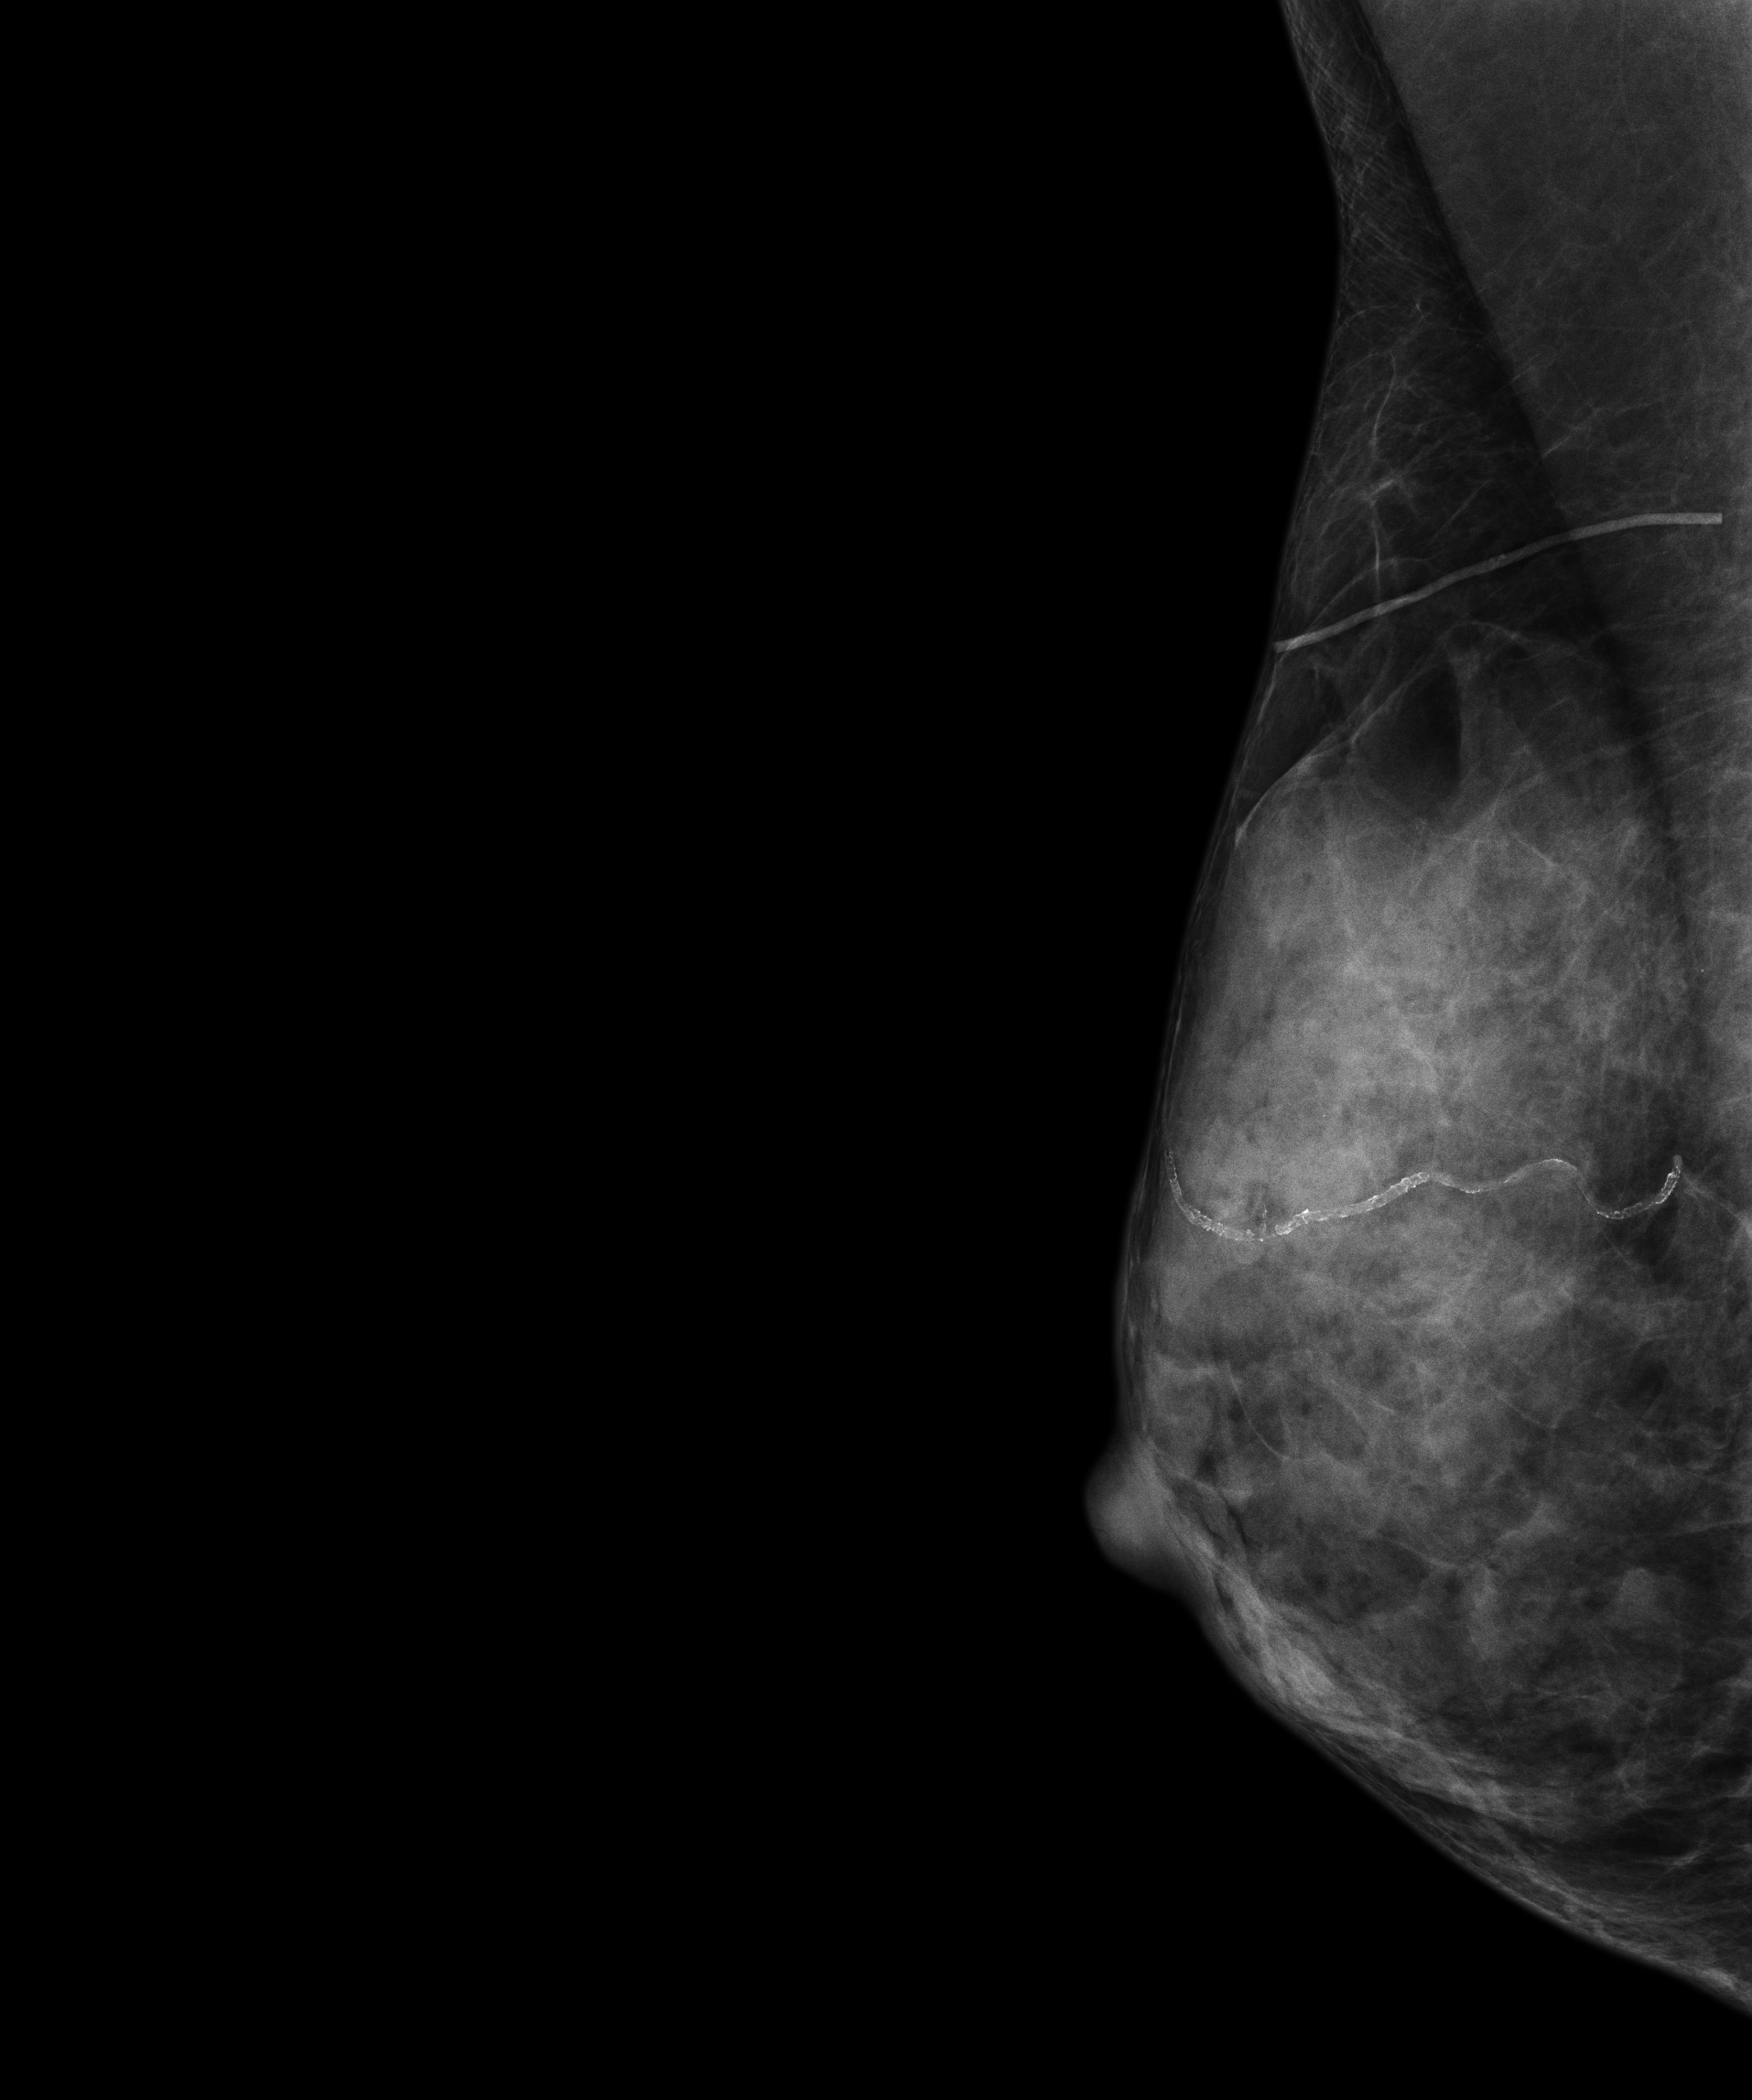
Annual screening mammography examination, system: Senographe Essential ADS_56.21.3. Female patient, age 59 years.
Image type: full-field digital mammogram. Breast: right. Projection: mediolateral oblique (MLO) view.